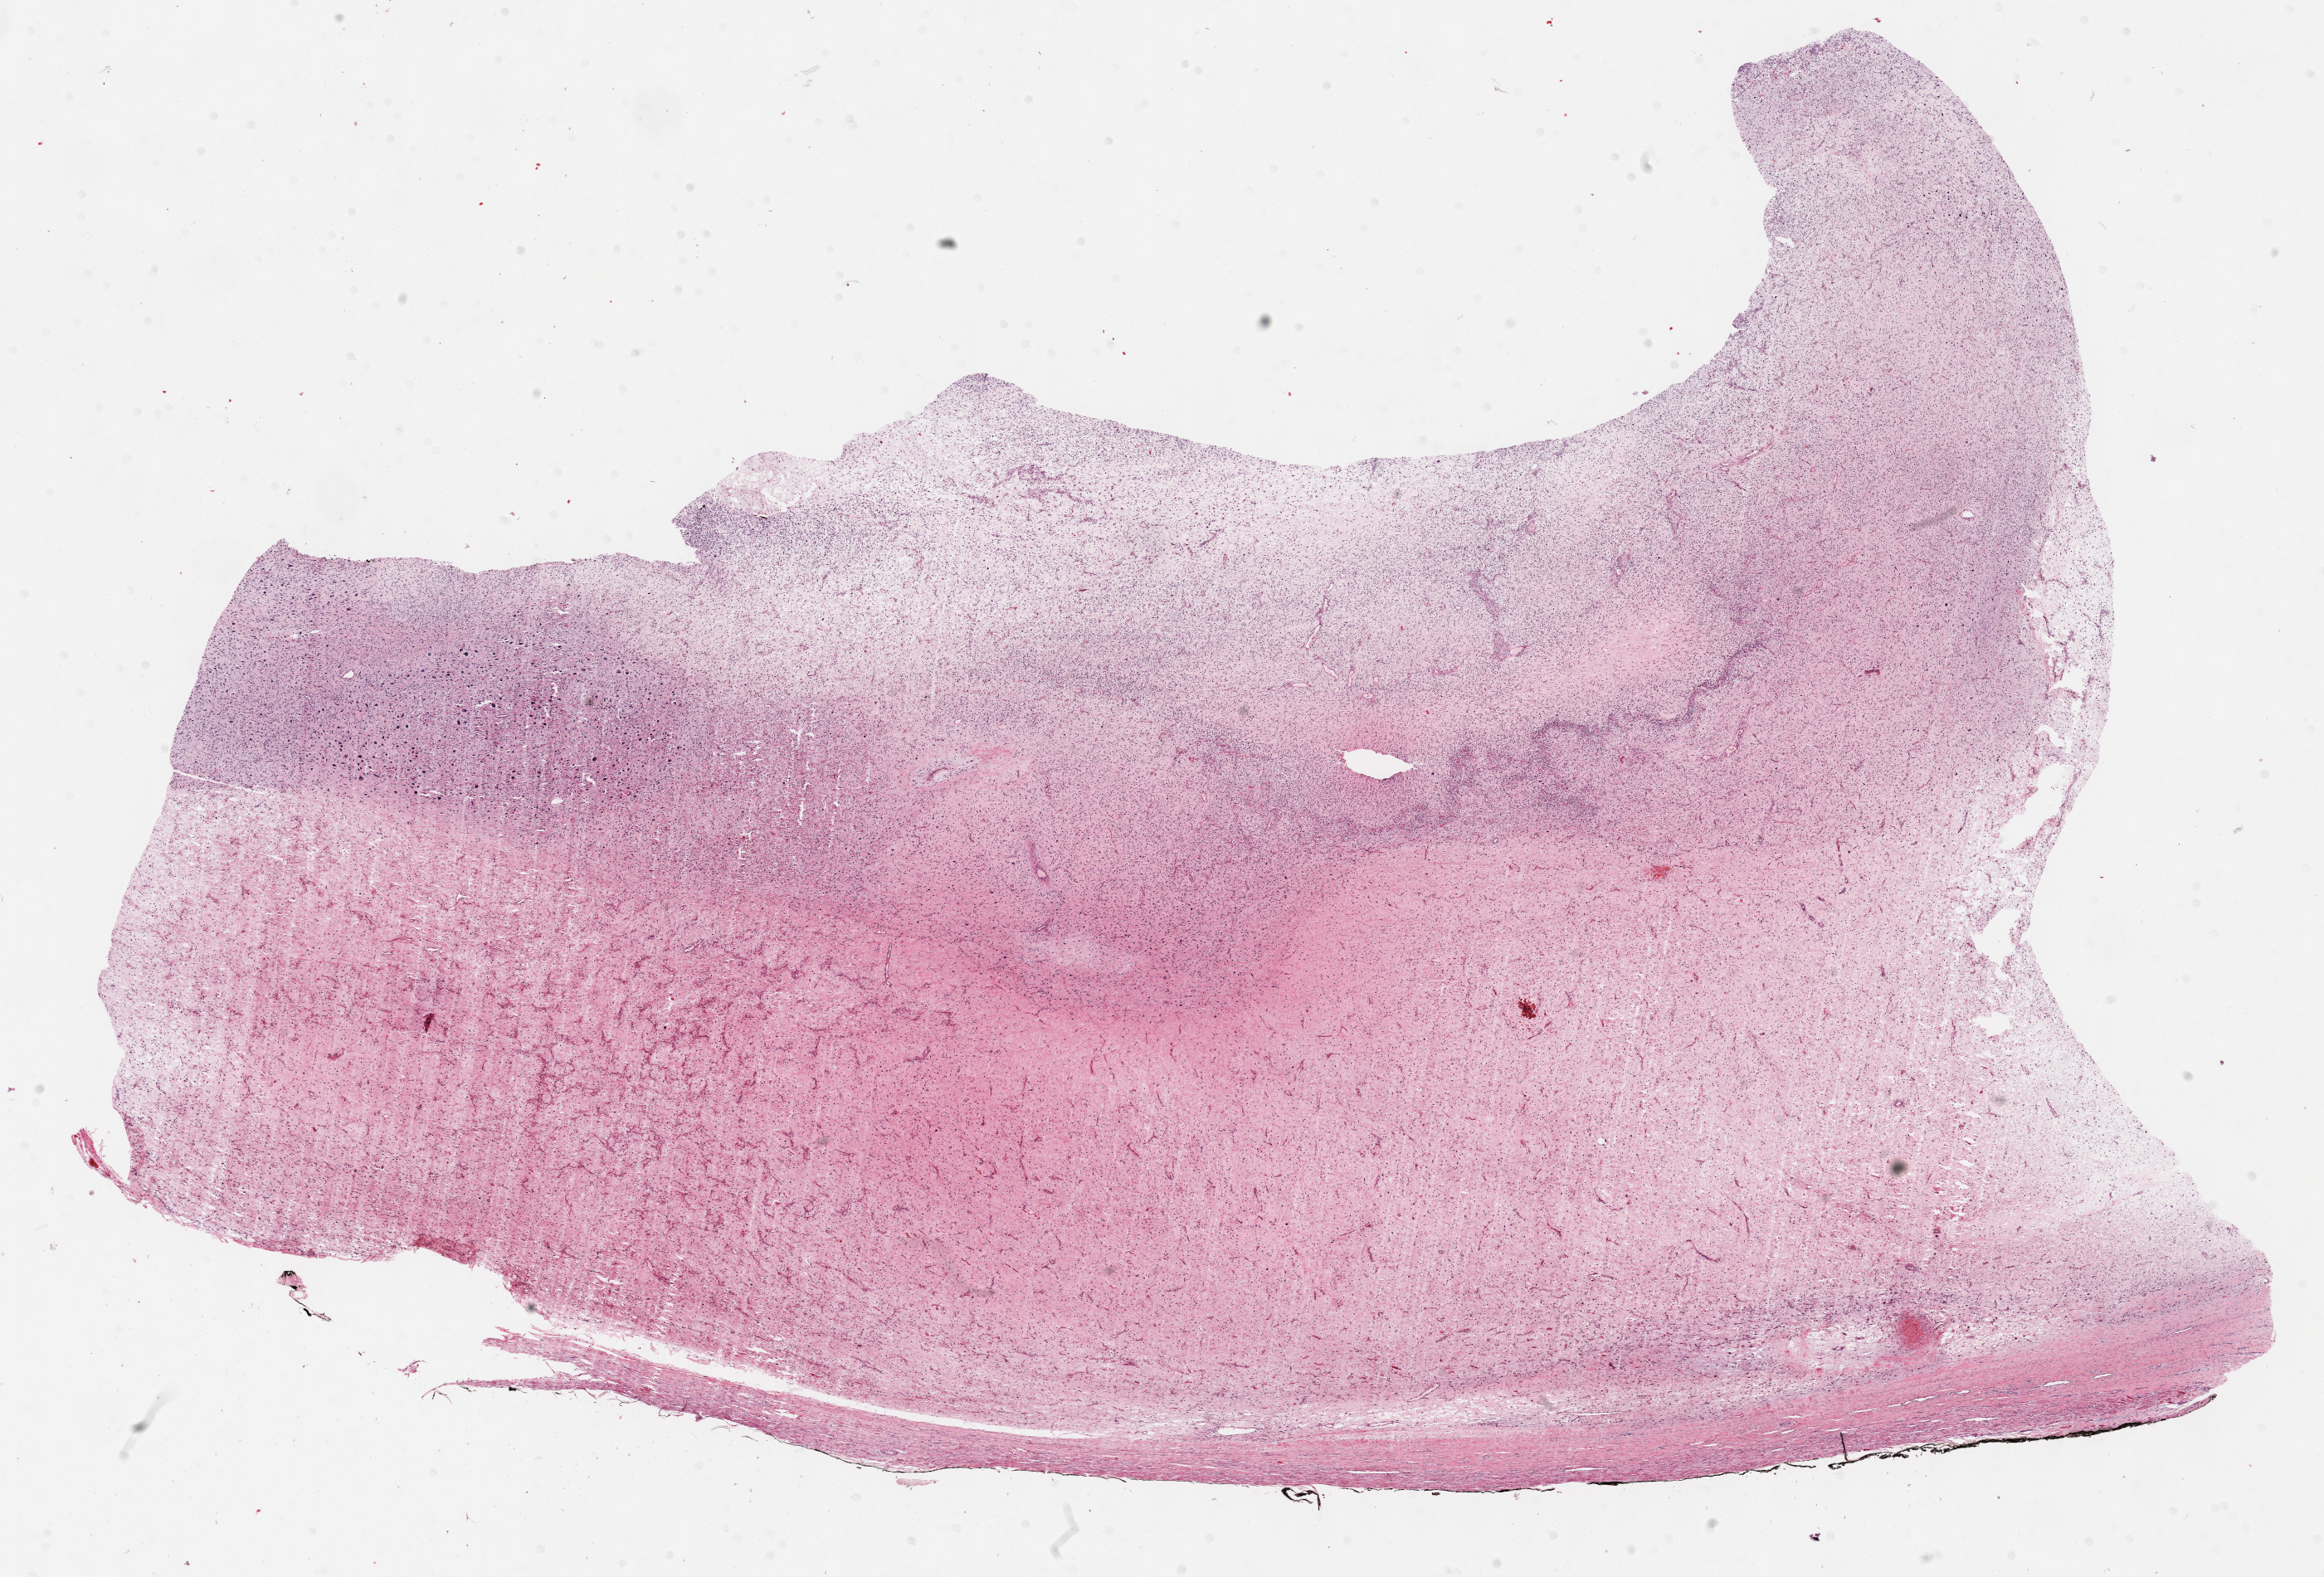
Whole-slide histology image, Hematoxylin and eosin (H&E) stained, shown as a low-resolution overview of the whole scanned area (about 22.7 x 15.4 mm, acquisition: 40x scan), FFPE section, primary tumour sample from the retroperitoneum and peritoneum. Male, age 57 years at initial diagnosis.
Histologic diagnosis: Fibromyxosarcoma (retroperitoneum).